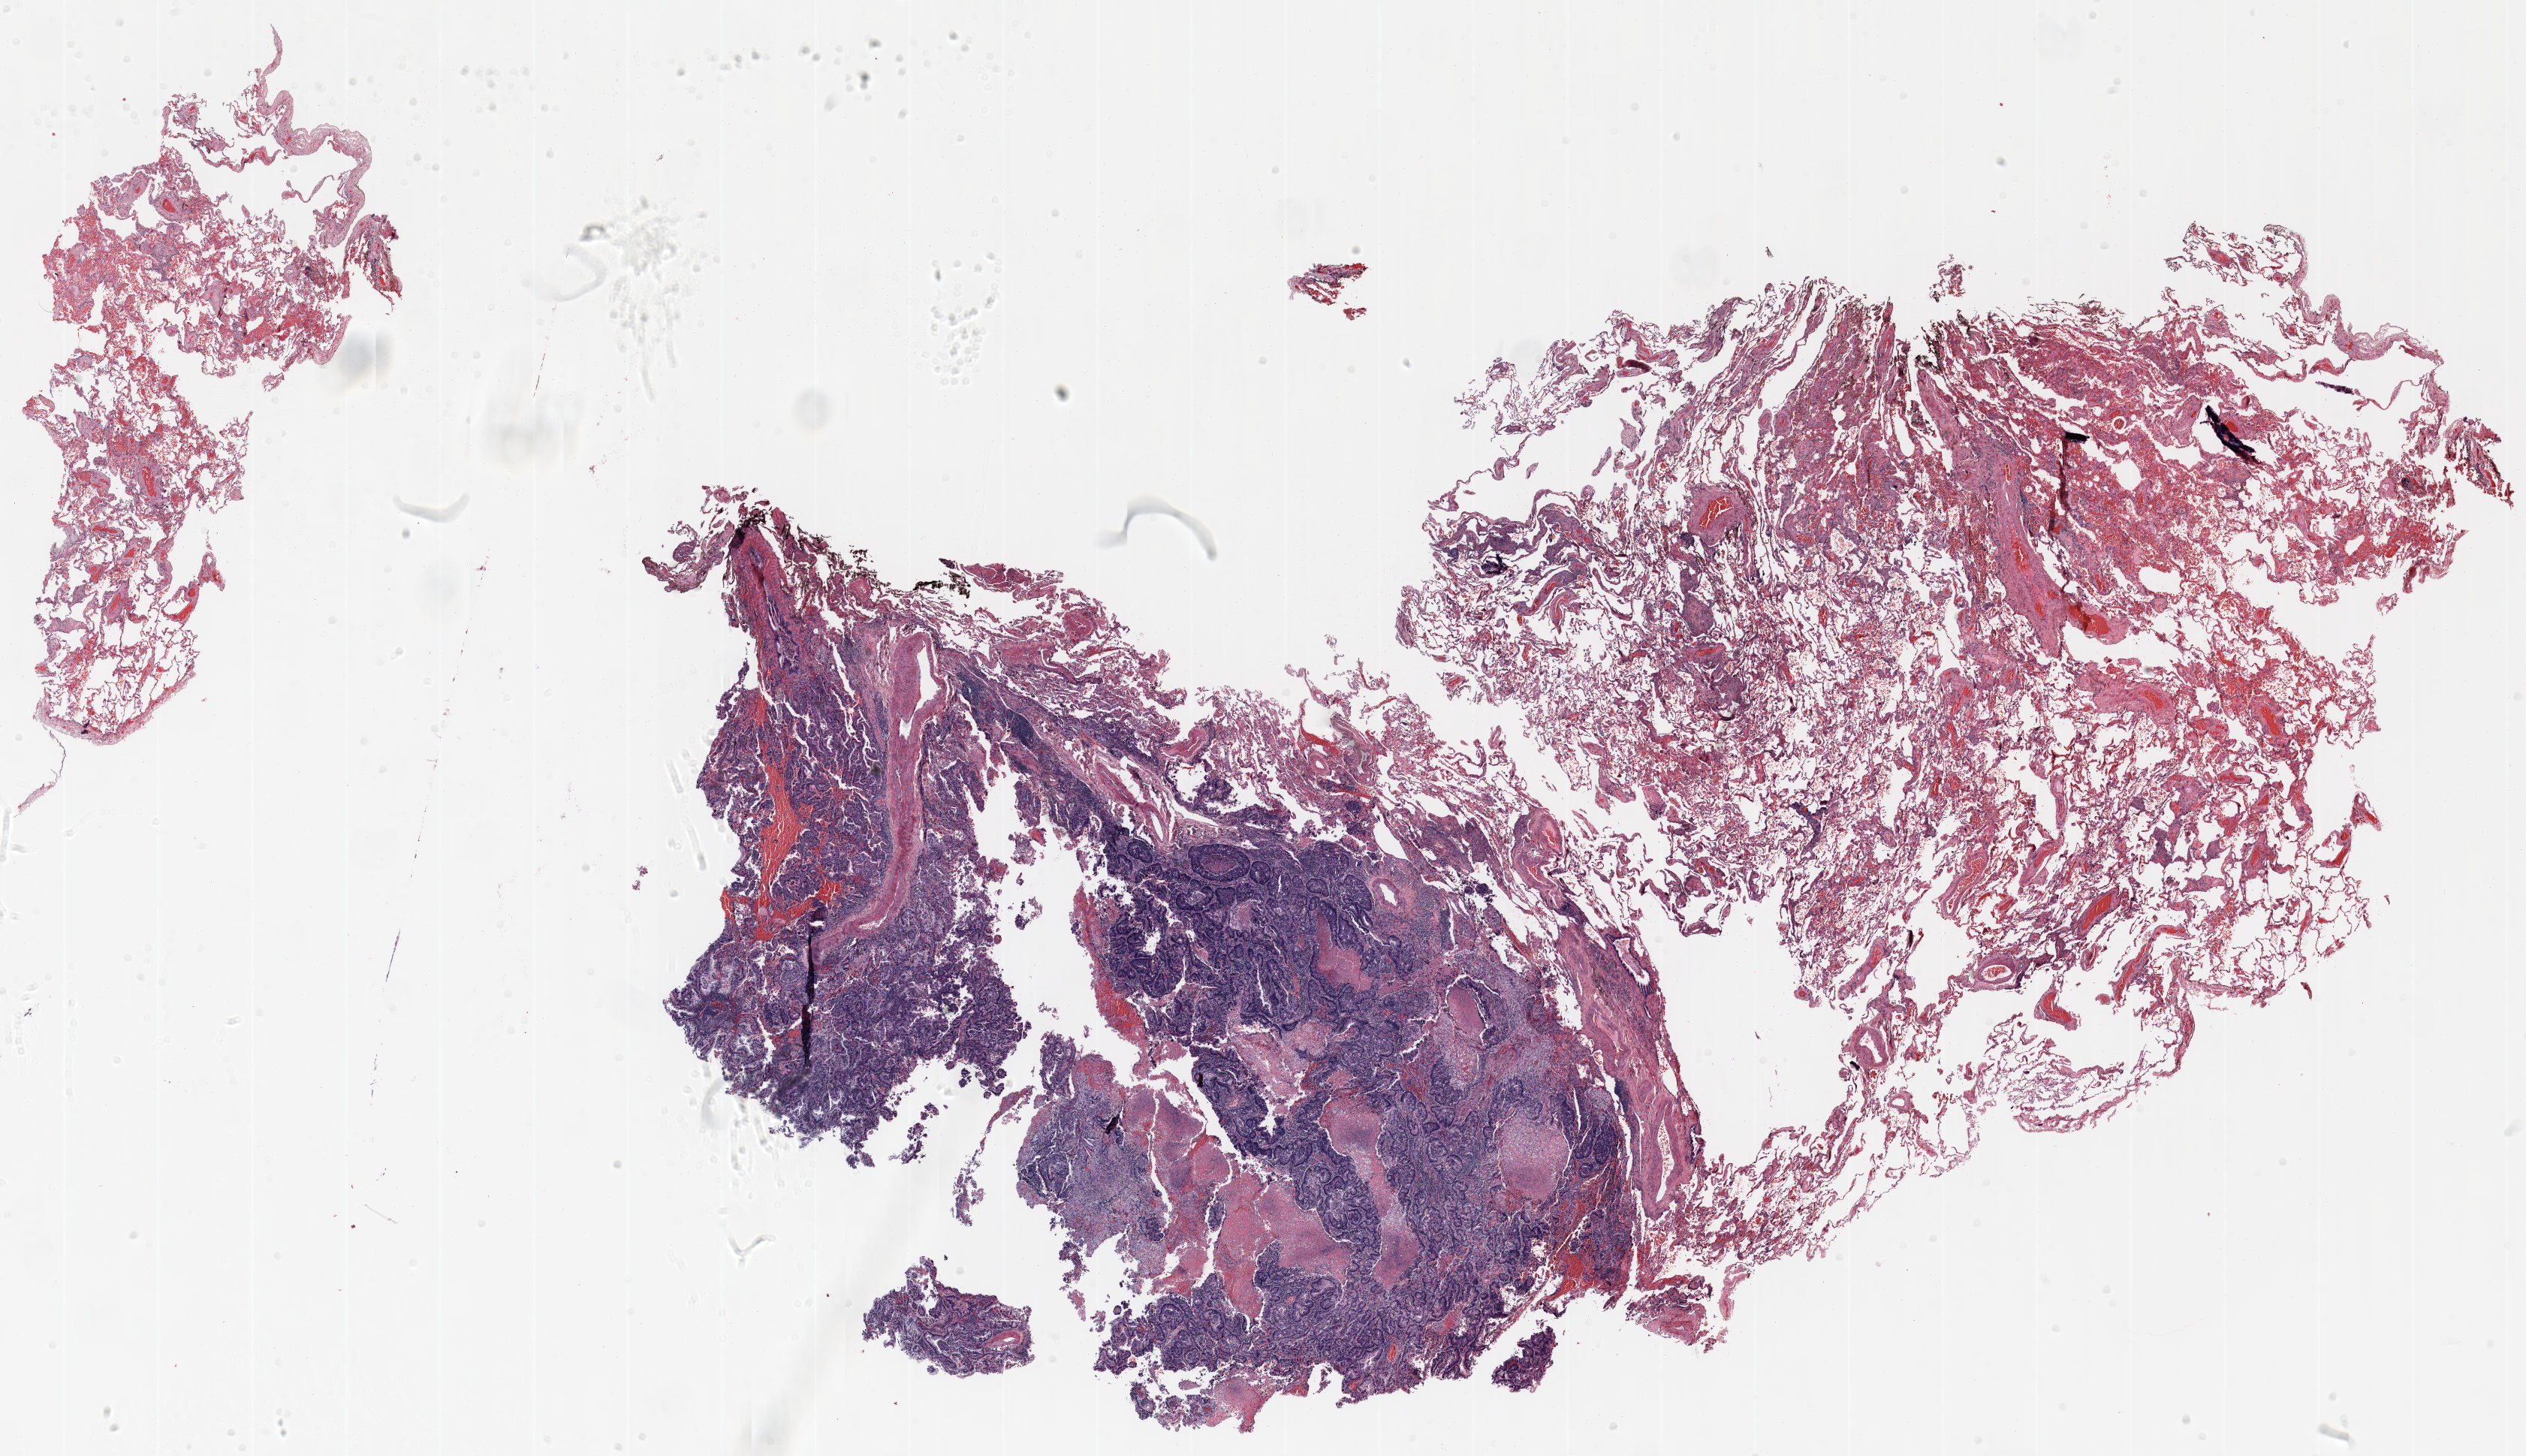
Whole-slide histology image, Hematoxylin and eosin (H&E) stained, low-resolution overview of the scanned area, about 27.0 x 15.6 mm (acquisition: 20x scan), formalin-fixed paraffin-embedded (FFPE) section, lung. Male, age 65 at enrolment. Former smoker at enrolment. Grade: moderately differentiated (G2).
Stage (AJCC 6th edition): IA. Participant's lung-cancer diagnosis: Adenocarcinoma, NOS (ICD-O-3 8140/3). Tumour size (pathology): 16 mm. Primary tumour location (clinical record): right upper lobe.